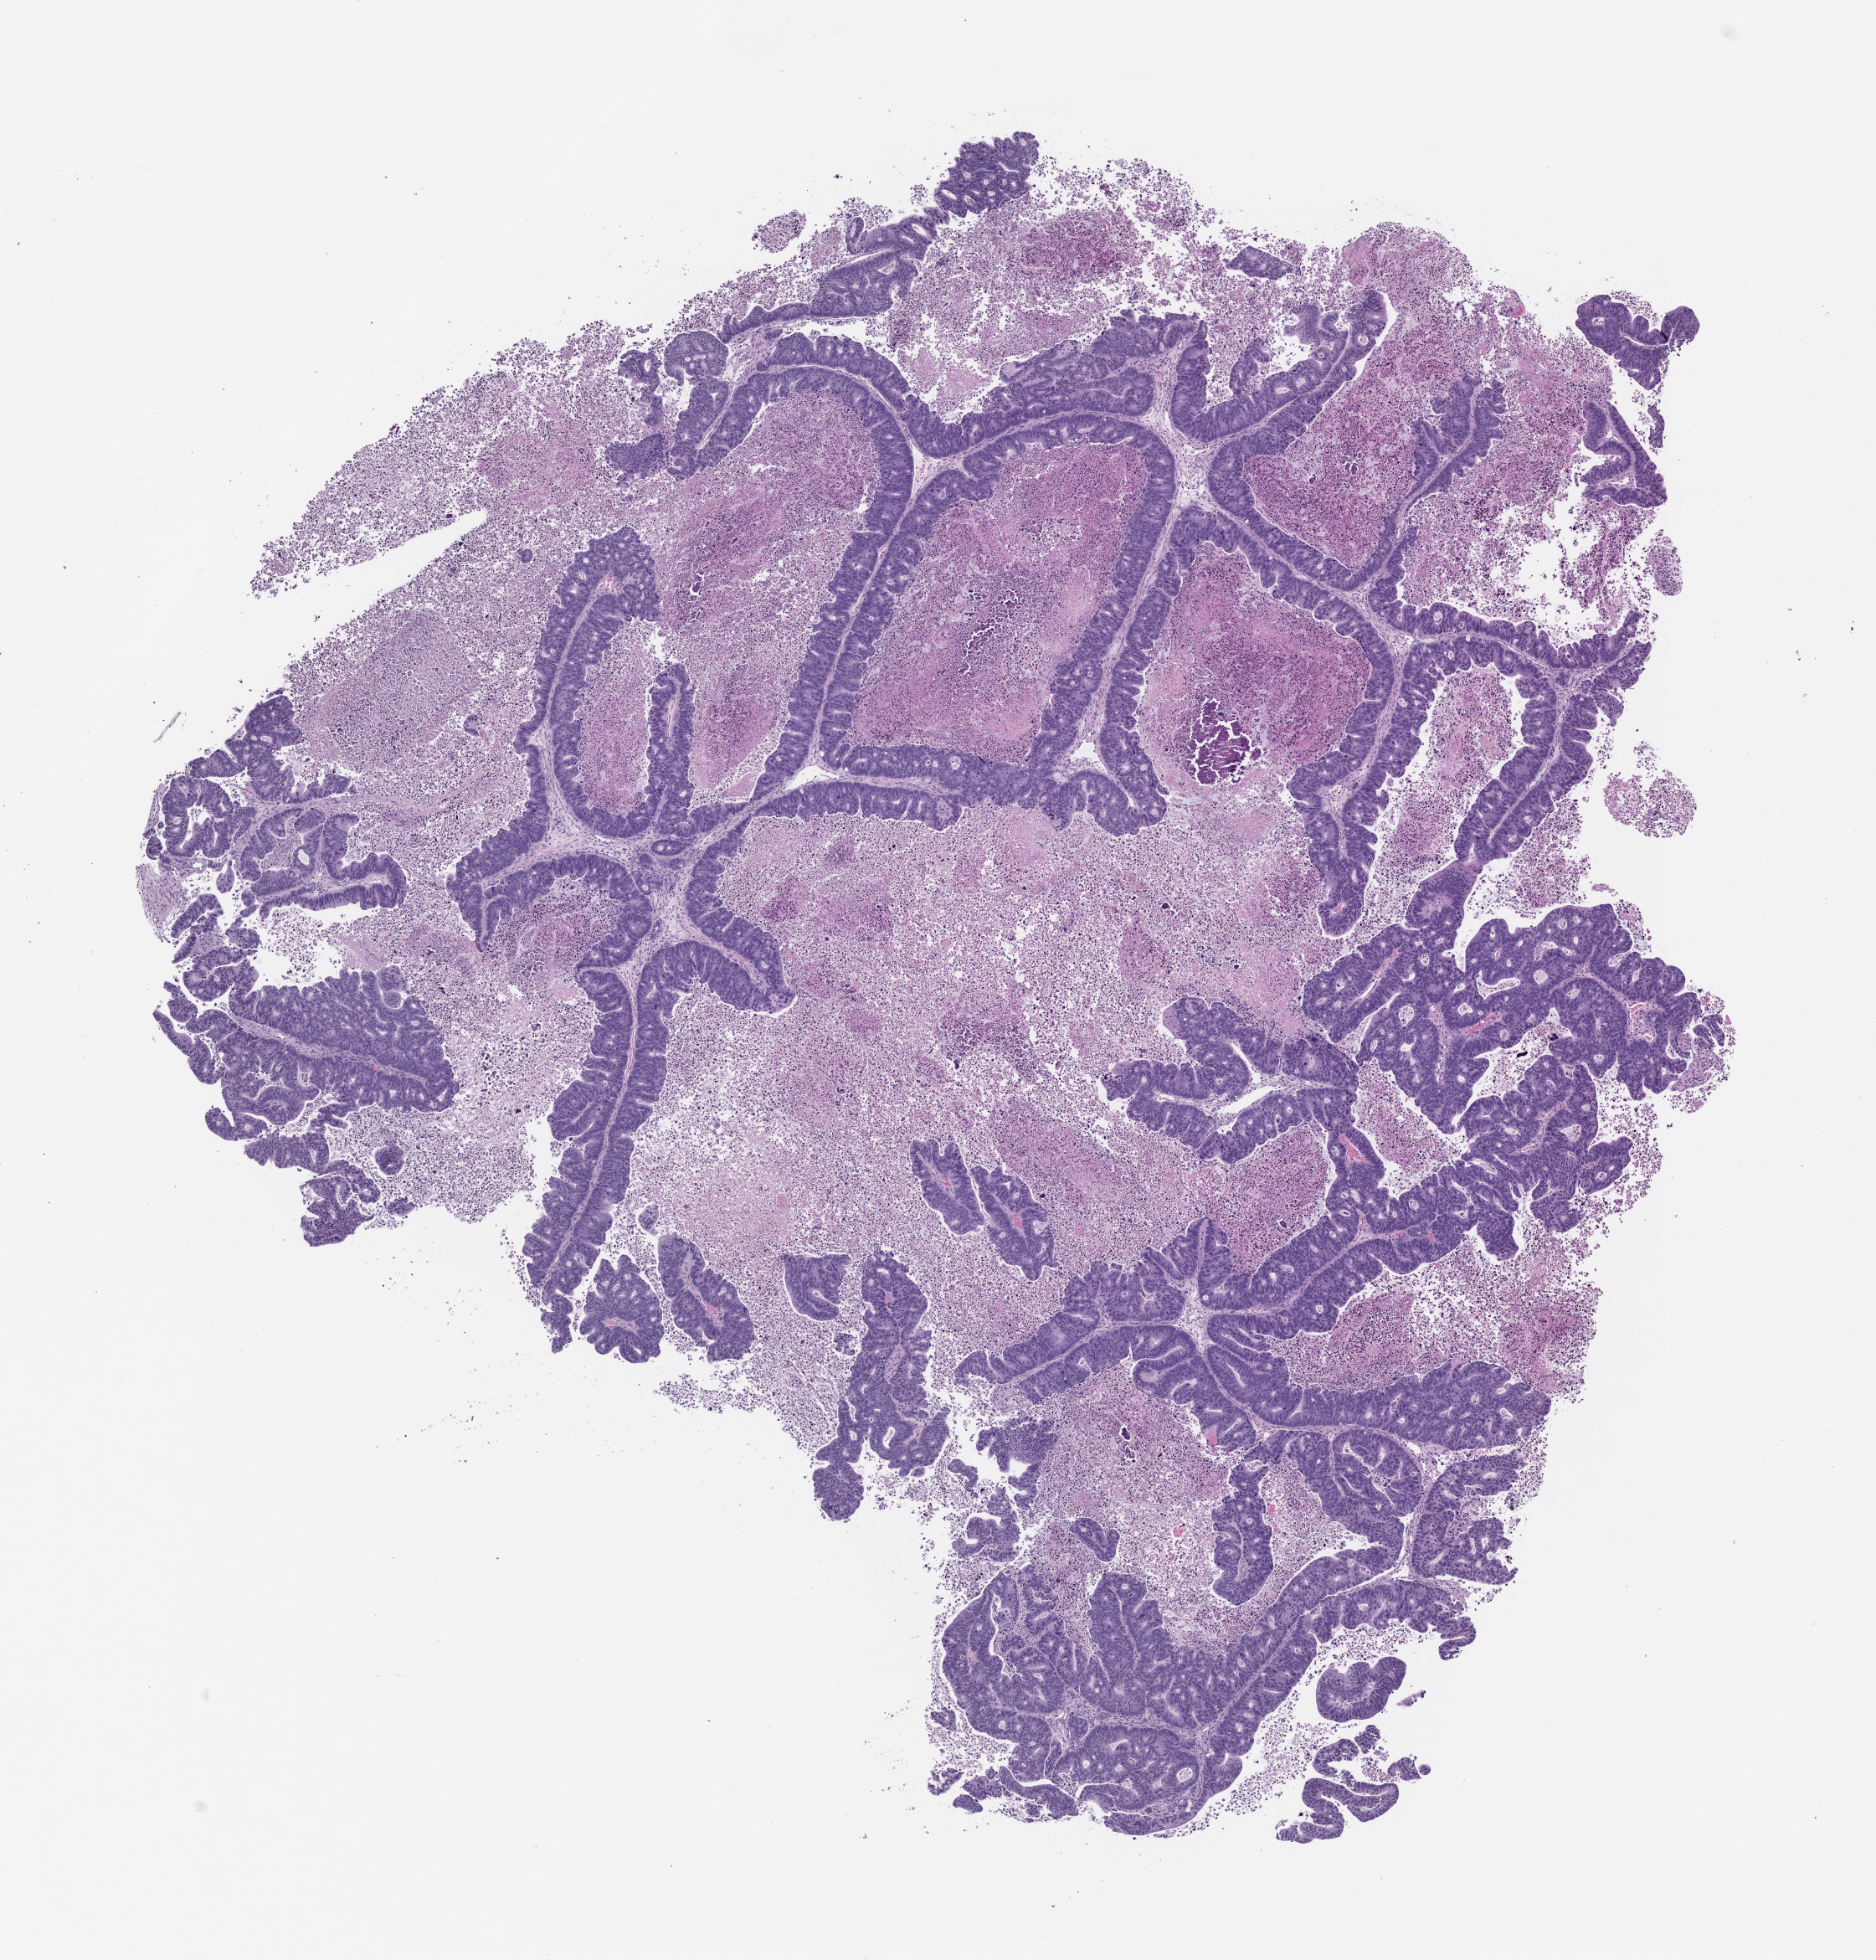
Whole-slide image, hematoxylin and eosin (H&E): patient-derived xenograft (human tumor grown in a mouse), passage 0, low-resolution overview of the scanned area, about 9.0 x 9.4 mm; FFPE section; tumor site category: colon.
Originating patient diagnosis: Colon Adenocarcinoma.